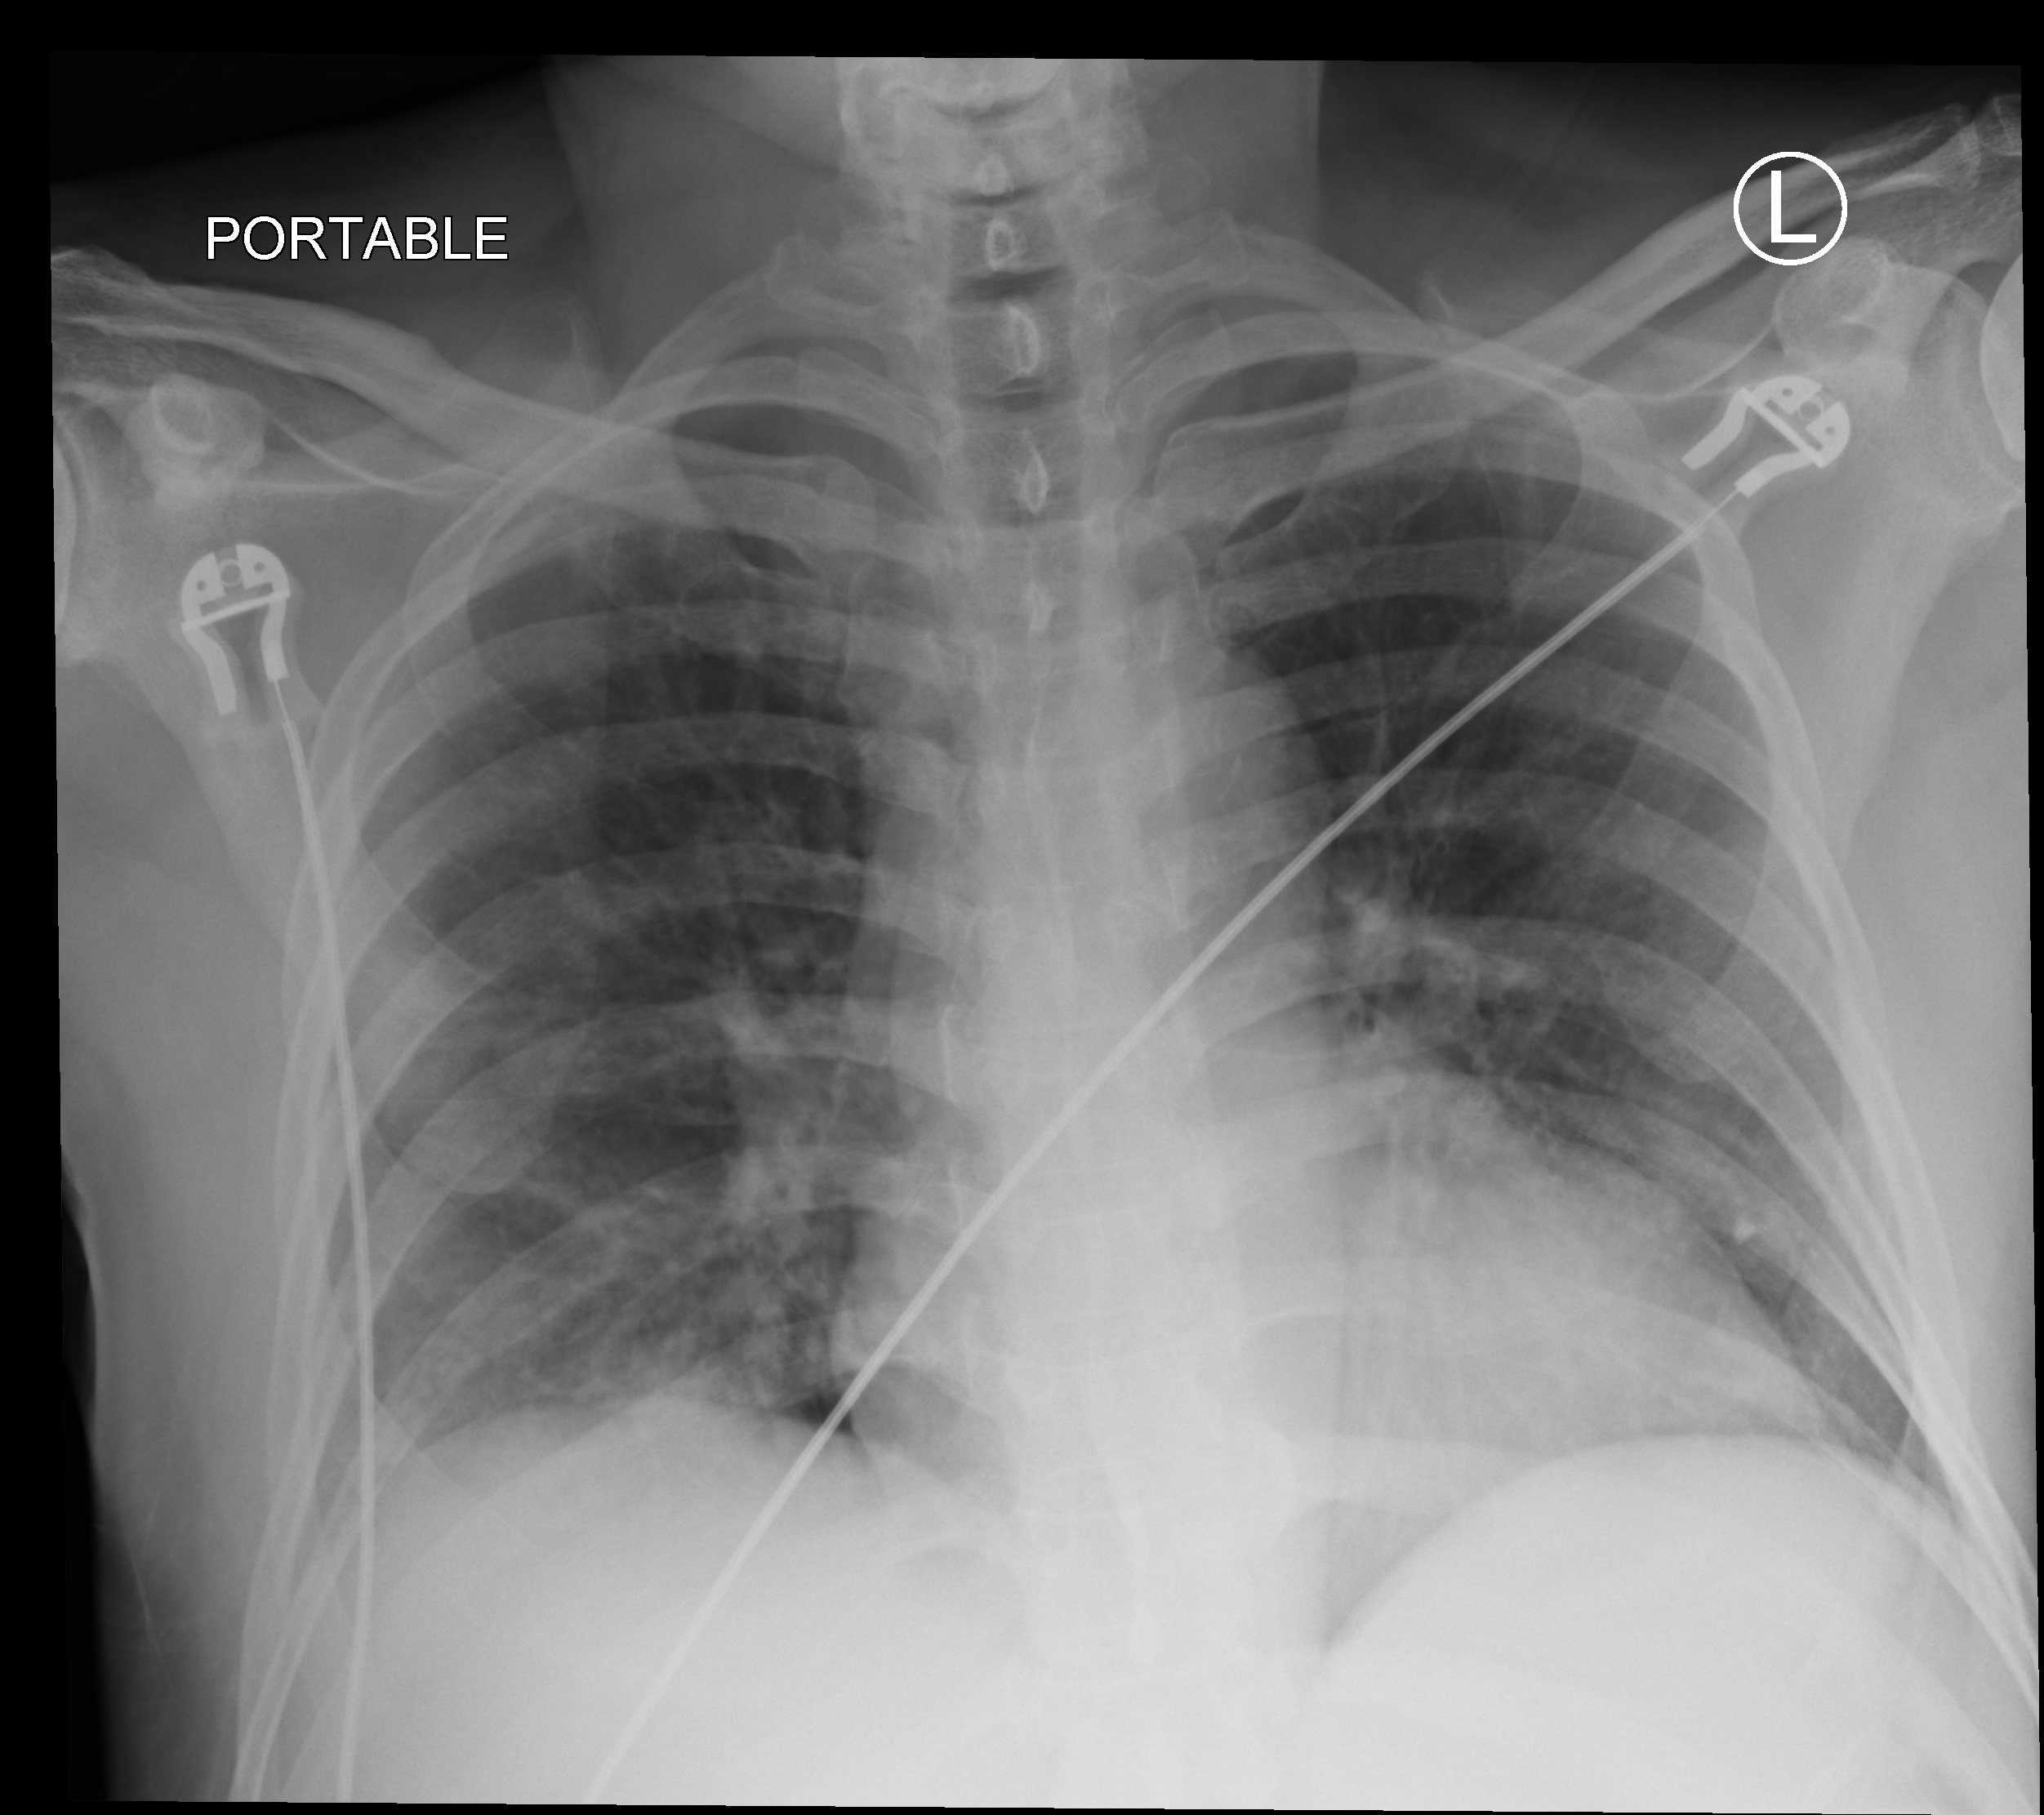
Chest X-ray (portable), anteroposterior (AP) projection. Male patient hospitalised with COVID-19, age 18–59 years.
Hospital-stay facts (about this admission, not read from this image; timing relative to this image not recorded): admitted to intensive care during this hospital stay: no.